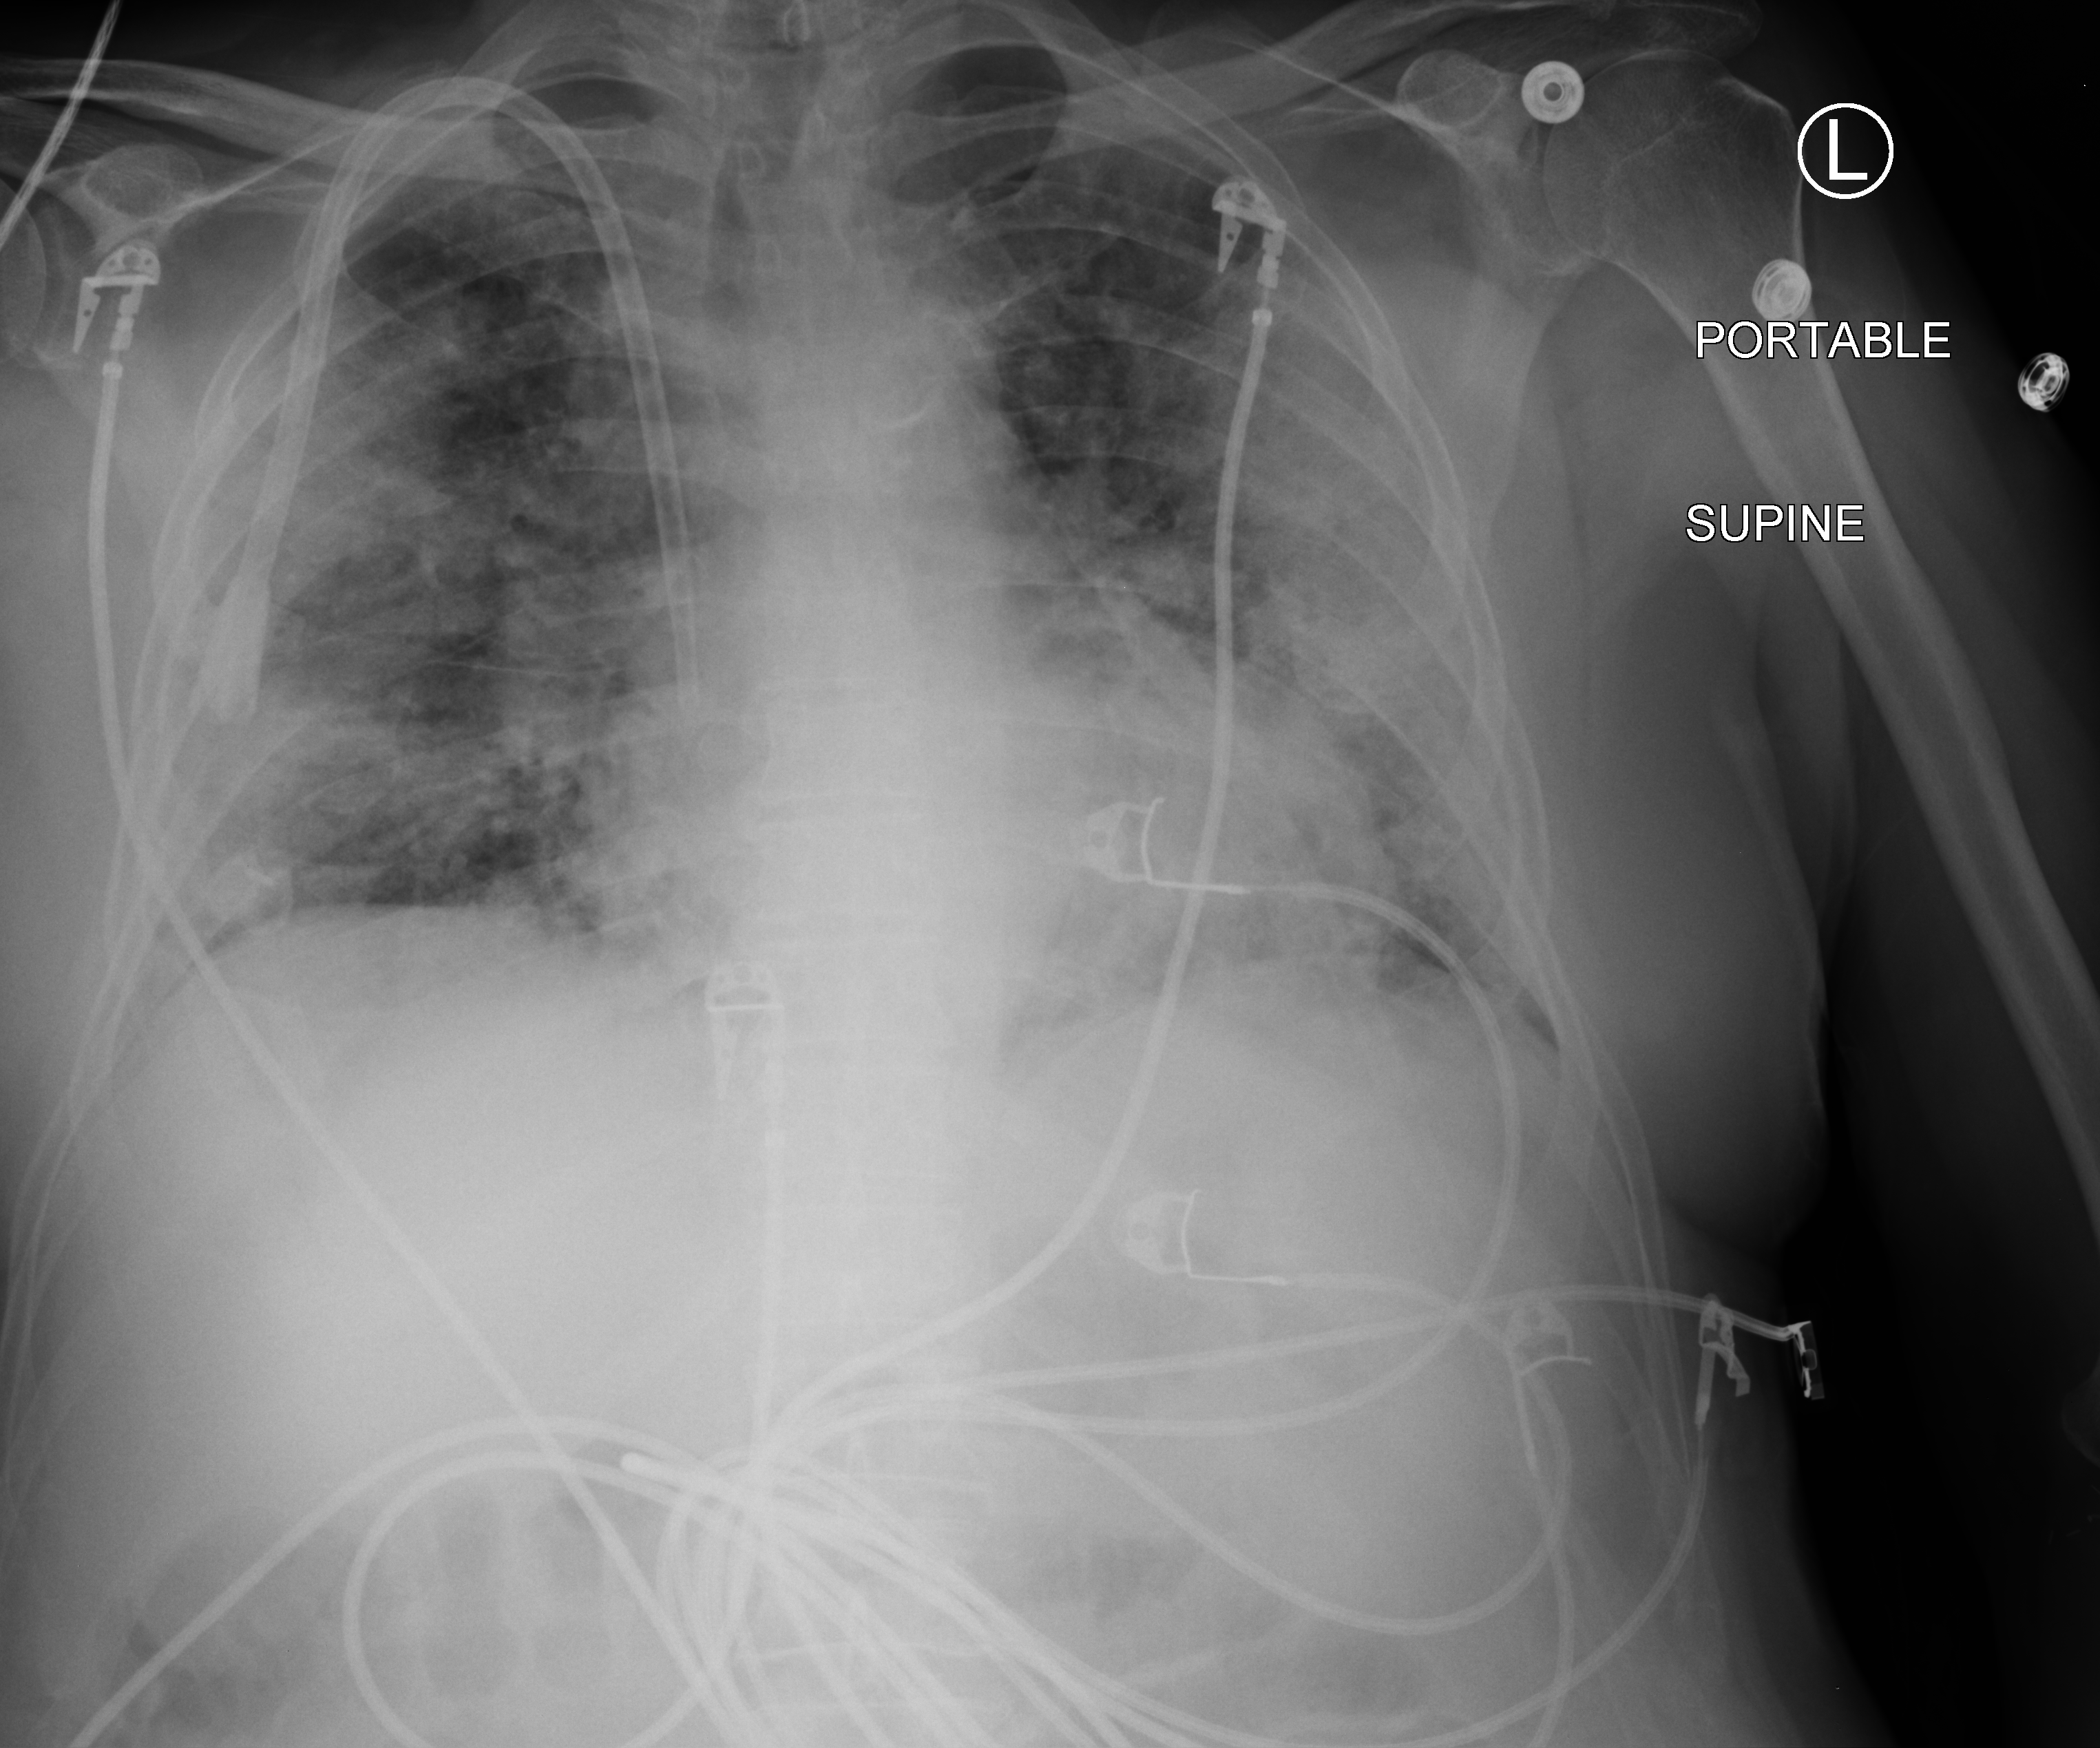
Bedside chest radiograph (computed radiography). Male patient hospitalised with COVID-19, age 60–74 years.
From the hospital-stay record, not from the radiograph (when in the stay this image was taken is not recorded): admitted to intensive care during this hospital stay: no; mechanically ventilated during this hospital stay: no.